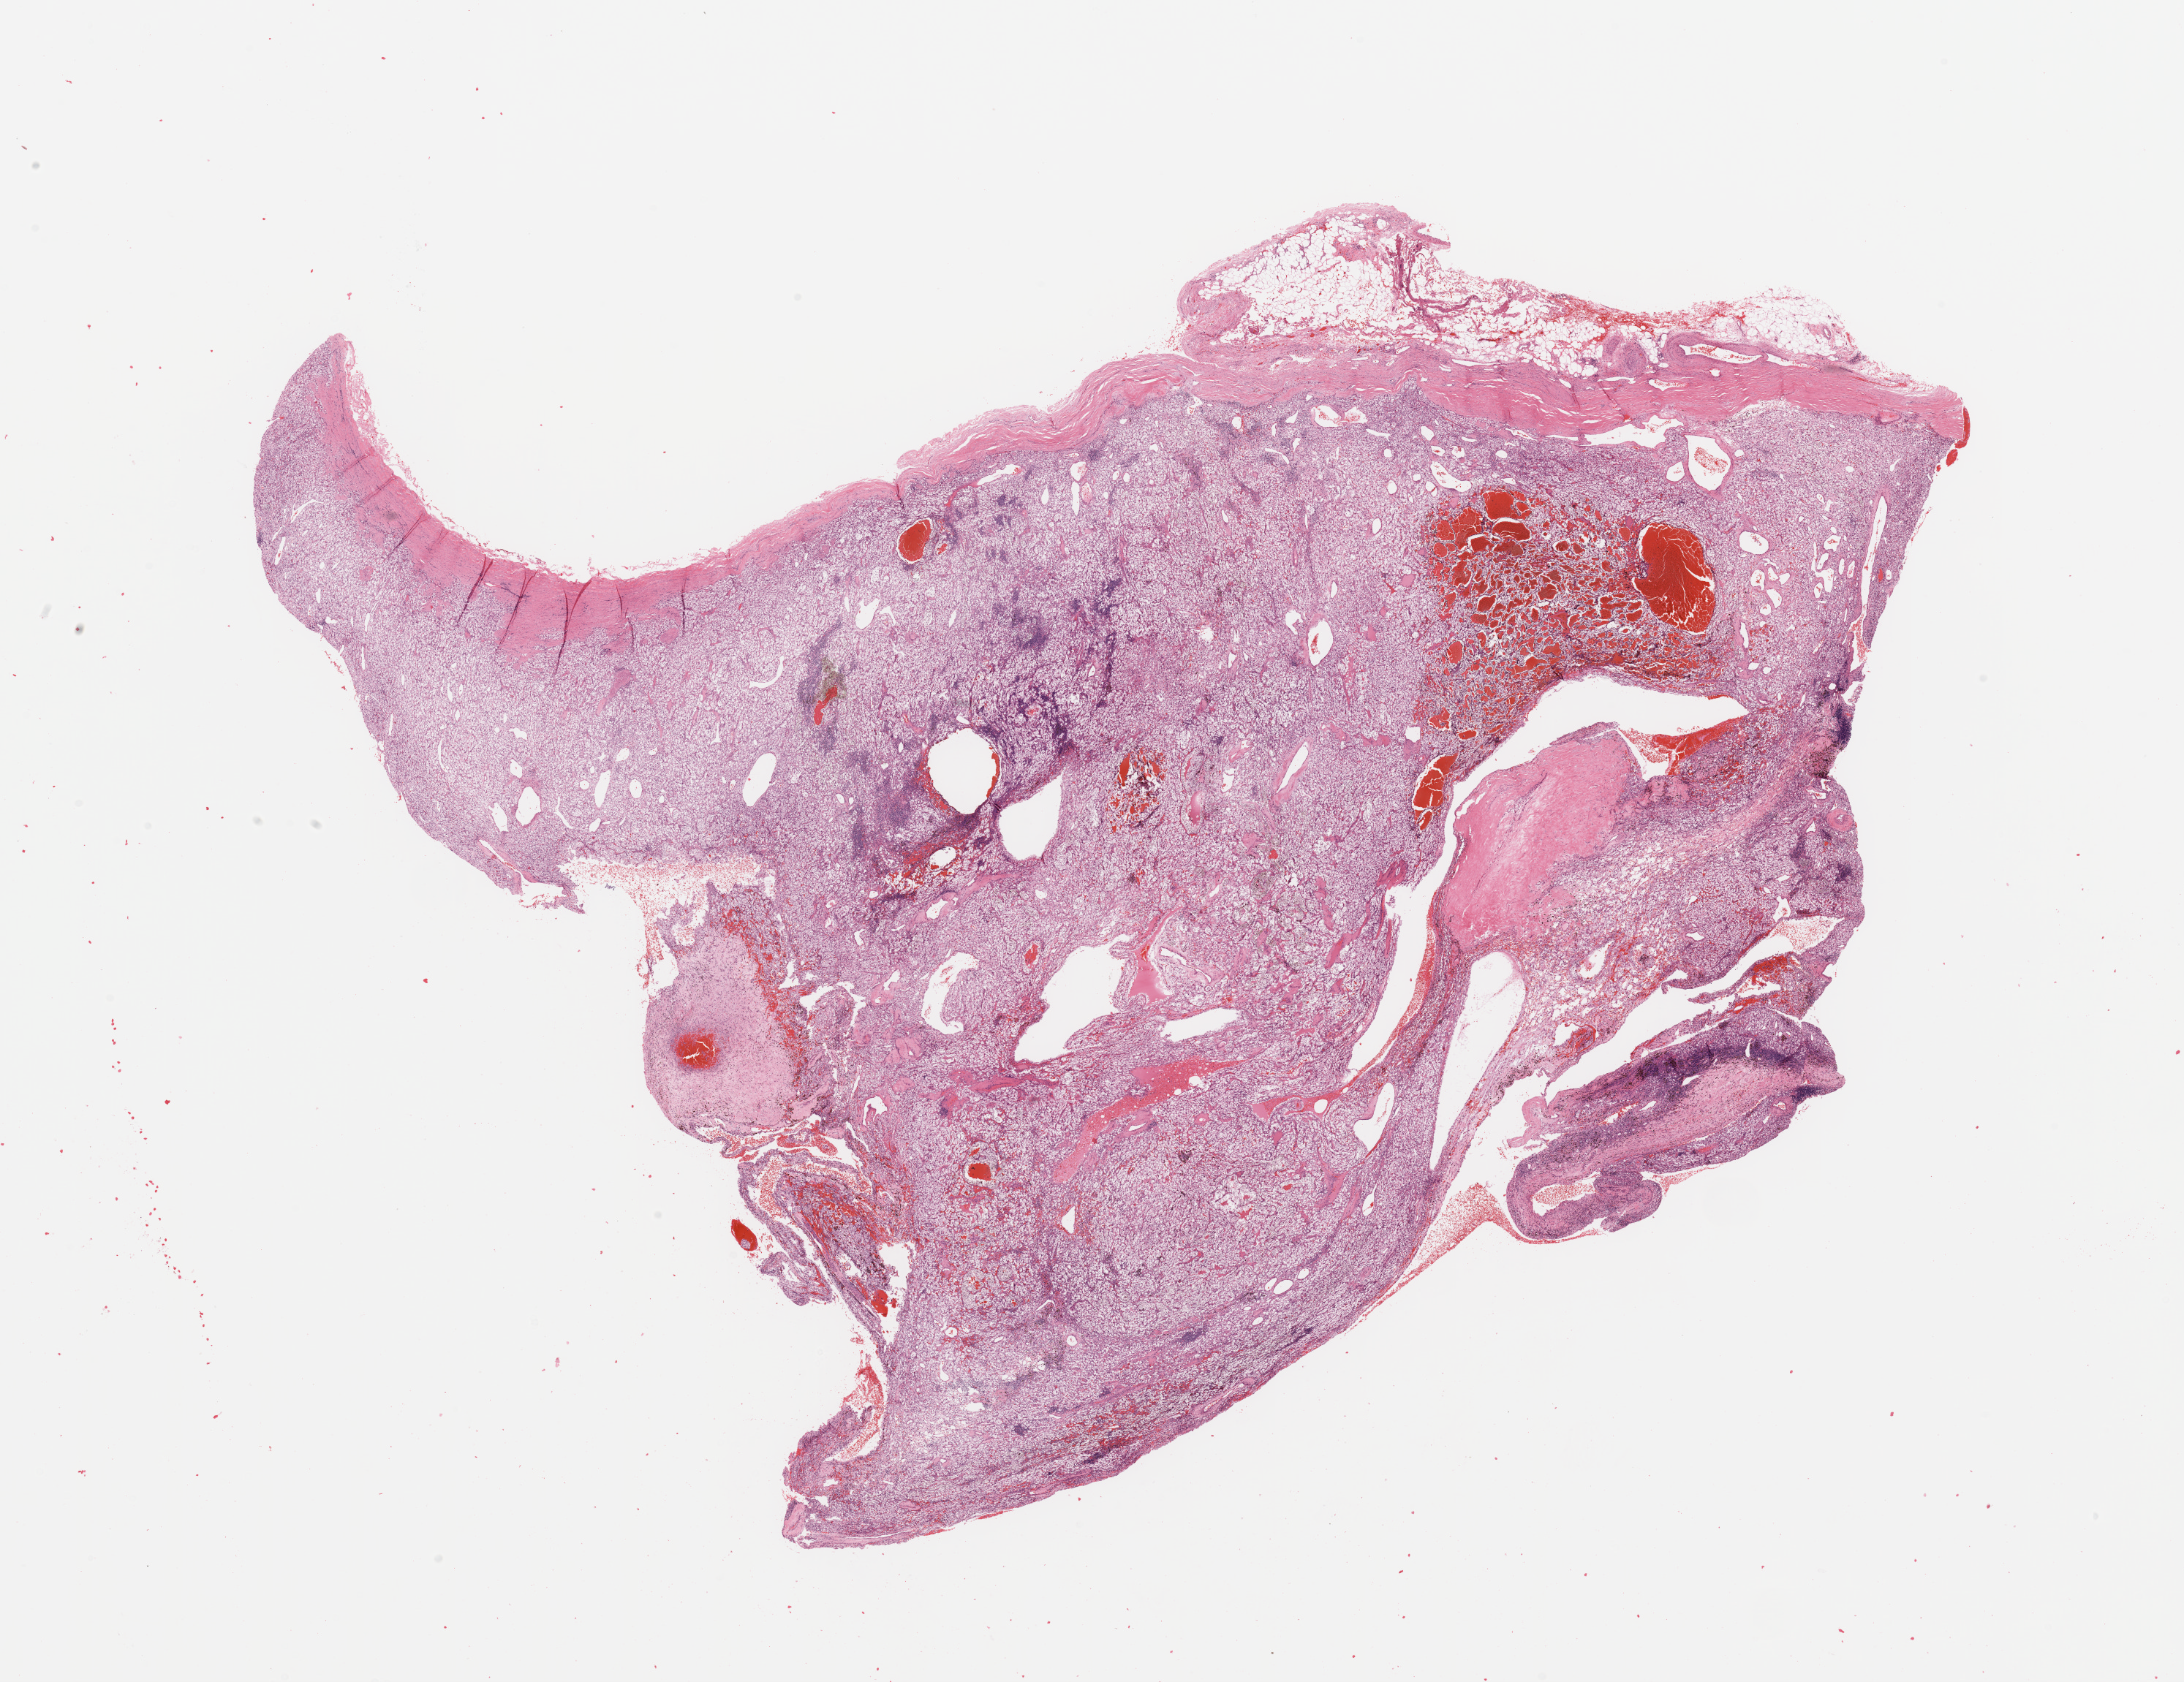
Hematoxylin and eosin (H&E) stained whole-slide image — low-resolution overview of the scanned area, about 23.6 x 18.2 mm (from a 20x scan), tumour tissue sample, sampled site: kidney. Male, 61 y/o. Composition of this section per pathologist review: tumour nuclei 80%, necrosis 3%.
Histologic diagnosis: Renal cell carcinoma, NOS.